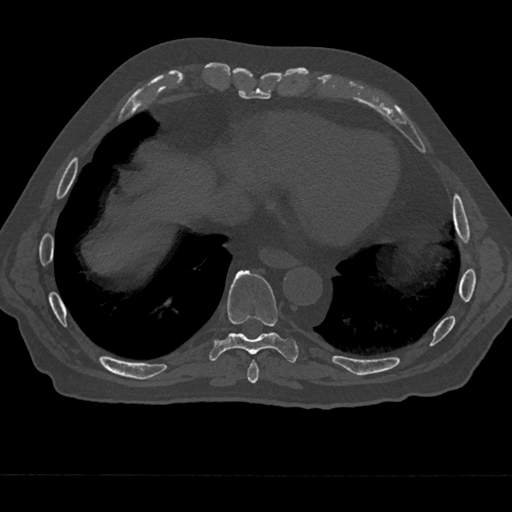
CT including the spine, one axial slice. Slice 261 of 797 in the series (ordered by position). 120 kVp. Bone window (W 1800 / L 400 HU). 512 × 512 image matrix. Male patient, age 75 years. From the clinical record (not read from this slice): primary cancer: renal; vertebrae with lytic lesions (as recorded): T4.
Structures marked on this image (semi-automatic segmentation, software-assisted and operator-edited):
- T8 vertebra: bounding box [x1, y1, x2, y2] px = [247, 358, 259, 384]
- T9 vertebra: [209, 271, 299, 363]